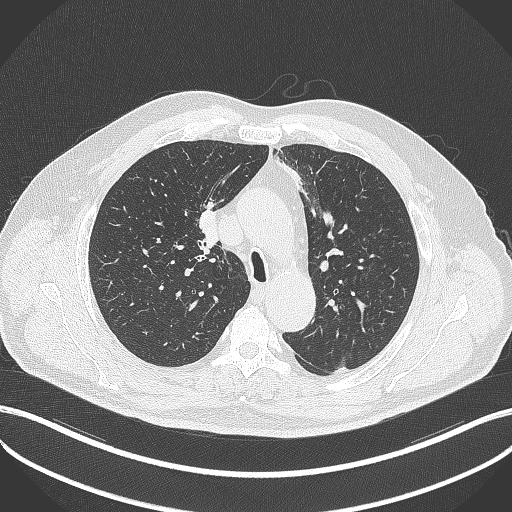
Chest CT, one axial slice. Slice 271 of 411 in the series (ordered by position). 120 kVp. Lung window (W 1500 / L -600 HU). 512 × 512 image matrix. Patient: male, 60 years. From the clinical record (not read from this slice): clinical TNM (as recorded): T1b N1 M0.
Outlined on this slice (bounding box drawn by a radiologist):
- lung tumour (recorded histology: squamous cell carcinoma): bounding box (x1, y1, x2, y2) in pixels: (191, 207, 225, 251)